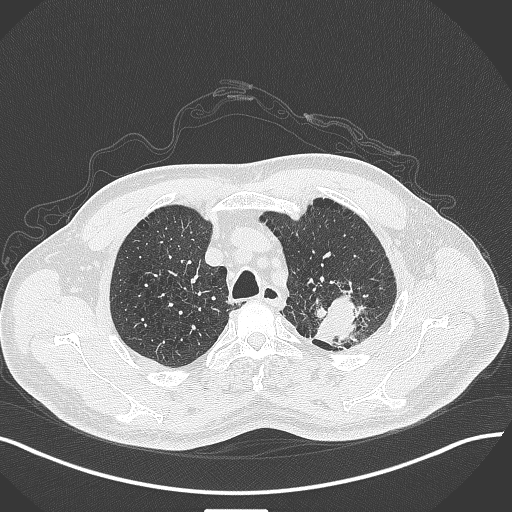
Chest CT, one axial slice; position 342 of 429 along the scan axis; 120 kVp; lung window (W 1500 / L -600 HU); 512 × 512 image matrix, field of view 400 × 400 mm. Male patient, age 55 years. Case-level facts recorded for this patient, not image findings: clinical TNM (as recorded): T3 N0 M1c.
Outlined on this slice (bounding box drawn by a radiologist):
- lung tumour (recorded histology: adenocarcinoma): box from (x=309, y=290) to (x=373, y=353) px